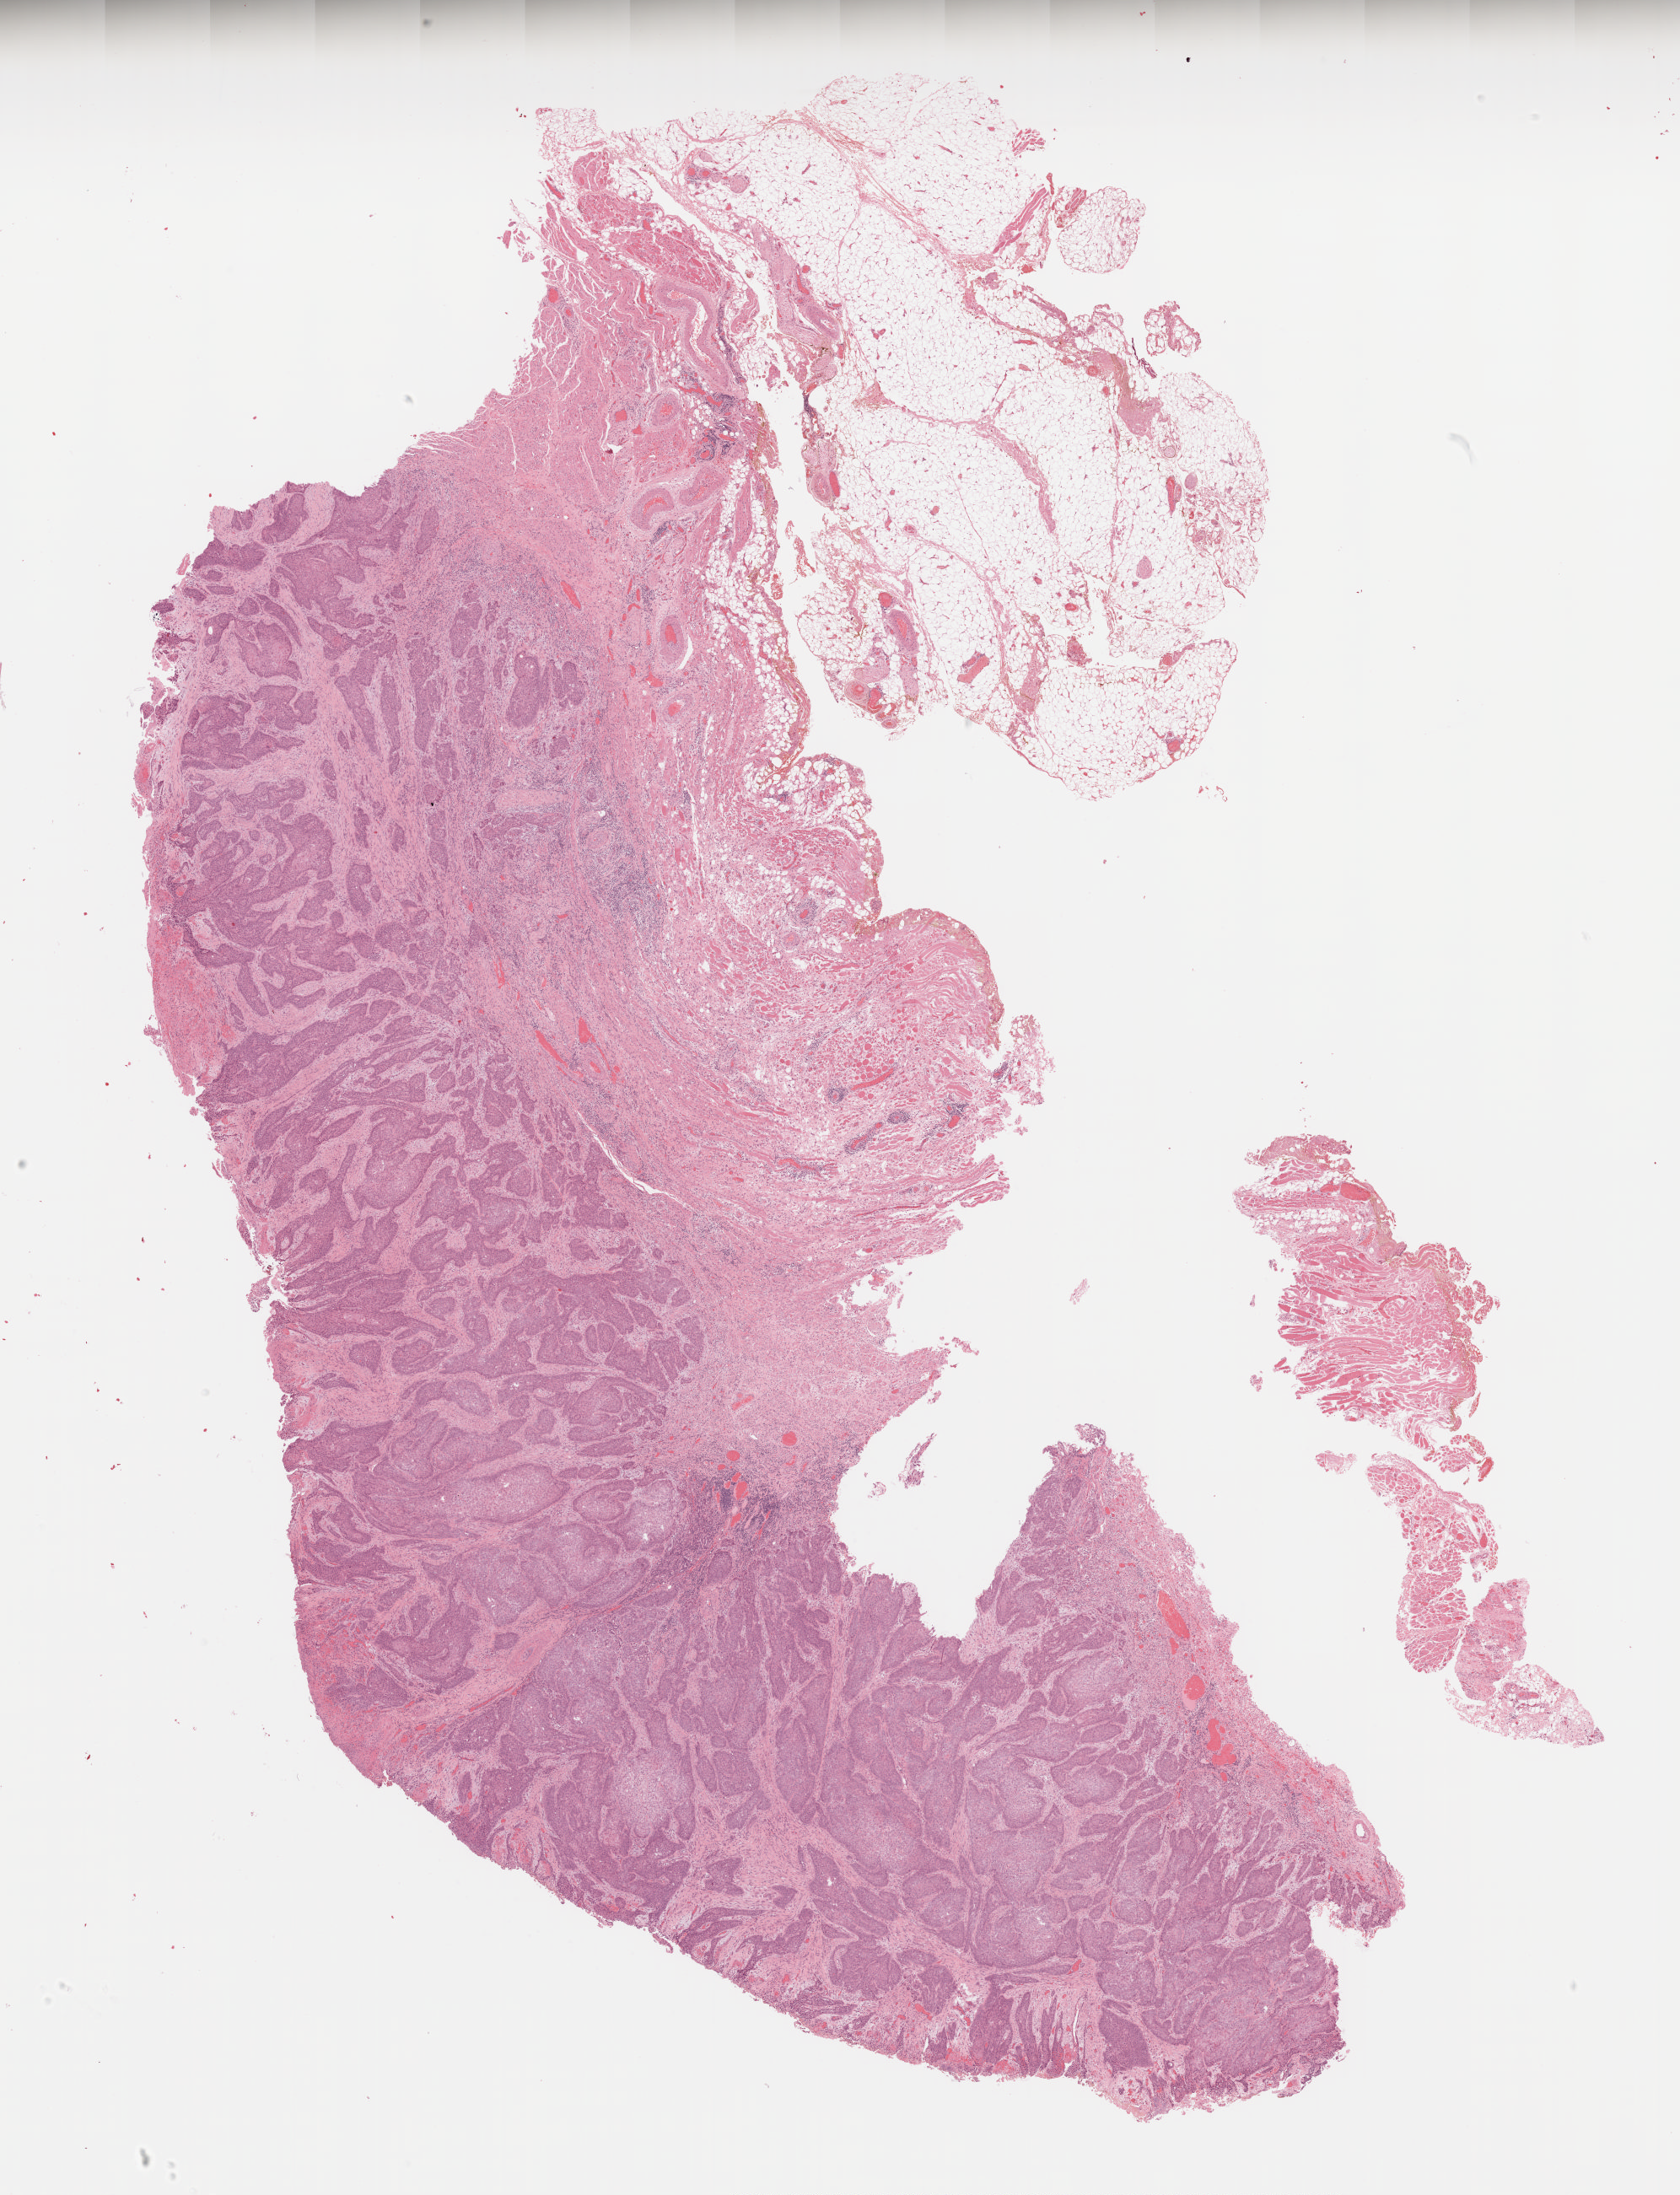
Digitized H&E-stained tissue section (whole slide) — a low-resolution overview of the entire scanned area, about 16.0 x 20.9 mm; FFPE section; head and neck, primary tumour sample. Female, age 78 years at initial diagnosis. Histologic grade: G2 (moderately differentiated).
Histologic diagnosis: Squamous cell carcinoma, NOS (cheek mucosa). Lymph nodes positive (case pathology): 0 of 16 examined. AJCC pathologic stage: III (7th edition).